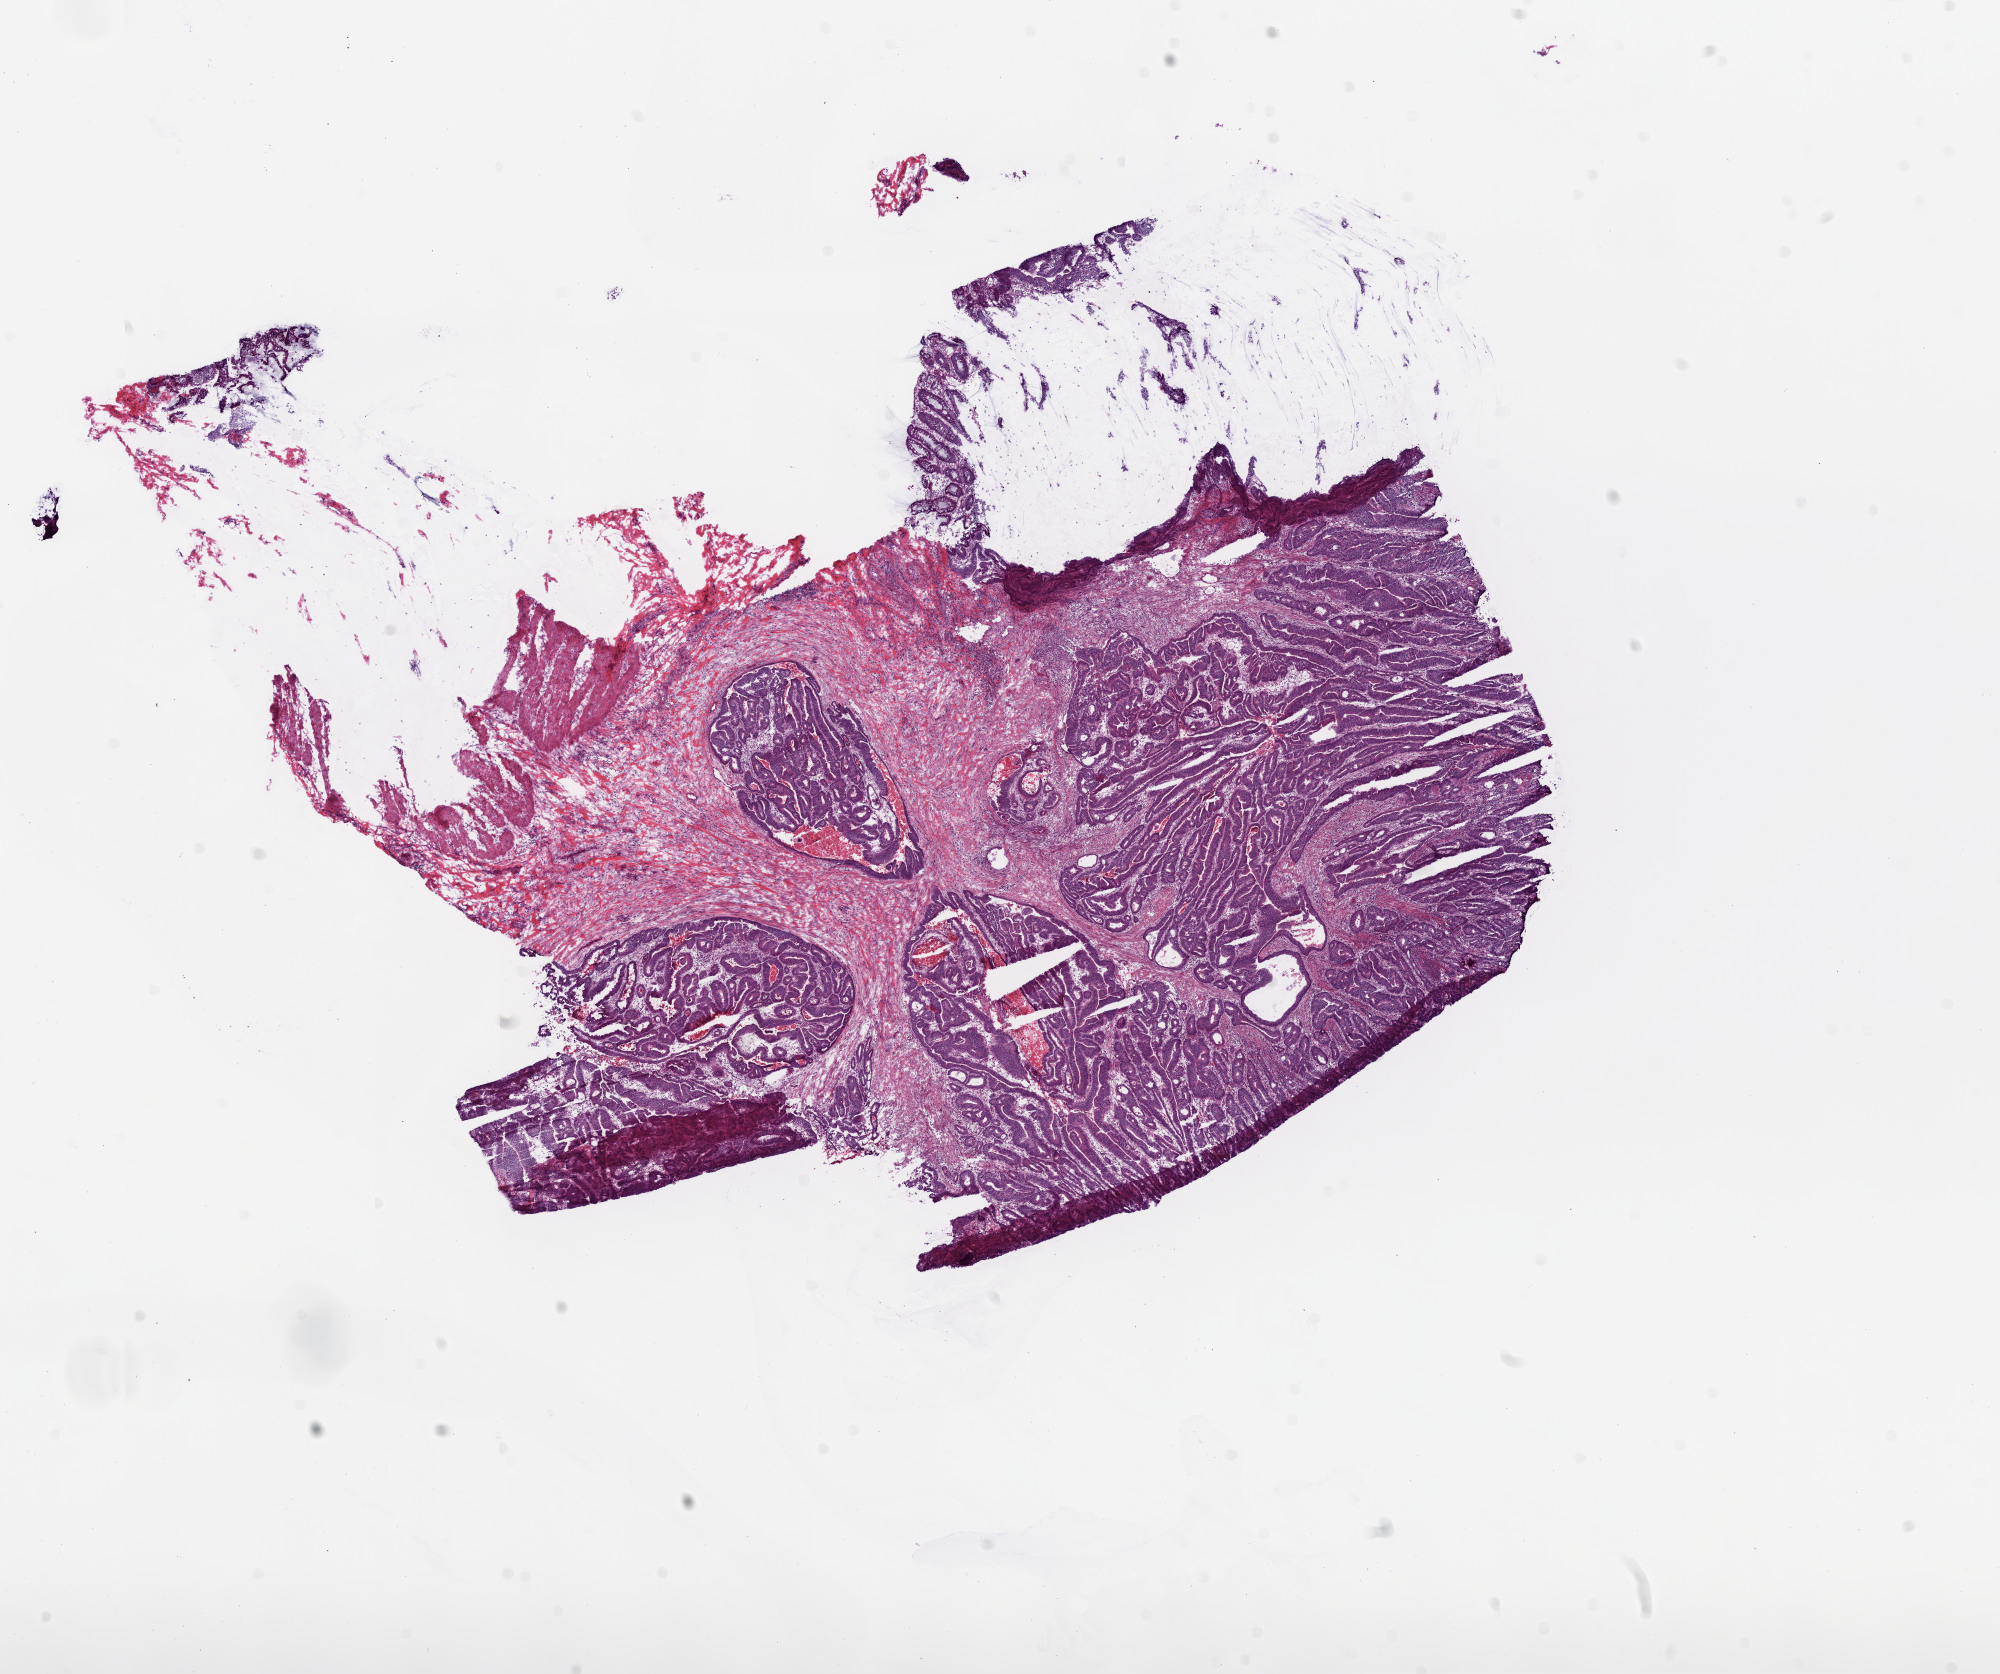
Whole-slide histology image, Hematoxylin and eosin (H&E) stained — low-resolution overview of the scanned area, about 16.0 x 13.4 mm, frozen section from the top of the tissue portion, sample: primary tumour, colon. Patient: male, age at initial diagnosis 77 years. Composition of this section per pathologist review: tumour cells 70%, tumour nuclei 80%, normal cells 2%, stromal cells 20%, necrosis 8%.
• AJCC pathologic stage: I (5th edition)
• TNM: T2 N0 M0
• lymph nodes positive (case pathology): 0 of 46 examined
• pathologic diagnosis: Adenocarcinoma, NOS